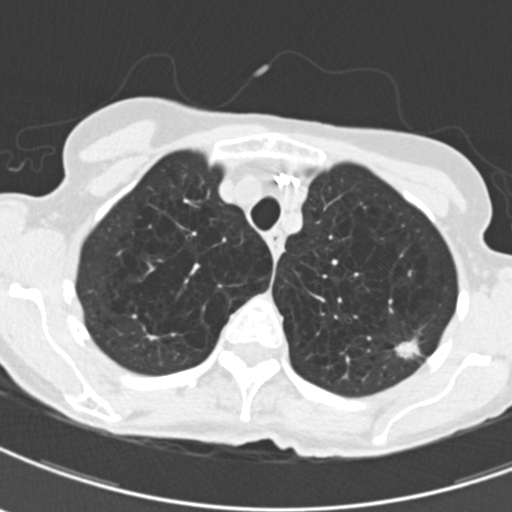
Low-dose screening chest CT, axial slice. Third screening round (two years after baseline). Lung window (W 1500 / L -600 HU). Slice 42 of 203 in the series. Female, age 71 years at enrolment.
Expert-annotated lung lesion, bounding box <389,326,435,368> (left, top, right, bottom; pixels). Screening reader's record for this exam (one nodule recorded; not confirmed to be the boxed lesion): non-calcified nodule or mass ≥4 mm, left upper lobe, 12 × 9 mm, spiculated (stellate) margins, mixed attenuation, pre-existing on the prior screen: yes; interval growth: yes. Participant outcome: lung cancer diagnosed 114 days after this screen — adenocarcinoma, NOS, left upper lobe, moderately differentiated (G2), stage IA (AJCC 6th edition), 12 mm at pathology.